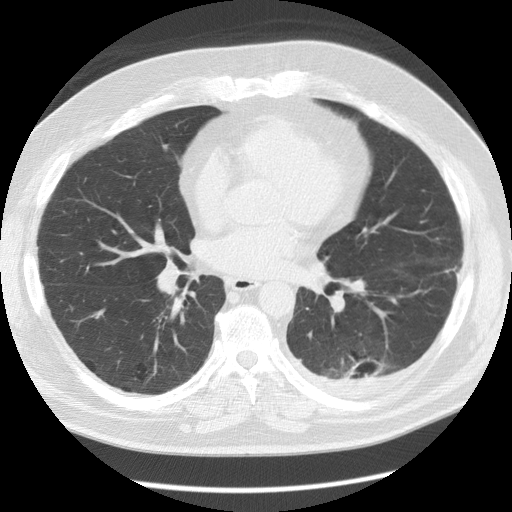
Axial slice from a low-dose chest CT screening exam, first (baseline) screen, lung window (W 1500 / L -600 HU). Male participant, aged 56 years at enrolment. Former smoker at enrolment.
• Expert reader's lesion annotation, bounding box [x1, y1, x2, y2] px = [325, 344, 398, 396].
• The screening reader recorded 4 non-calcified nodules or masses ≥4 mm on this exam (left lower lobe, left lower lobe, right middle lobe, left upper lobe); which of them this box marks is not recorded.
• Lung cancer was diagnosed 173 days after this screen: non-small cell carcinoma, left lower lobe, stage IV (AJCC 6th edition), 50 mm at pathology.